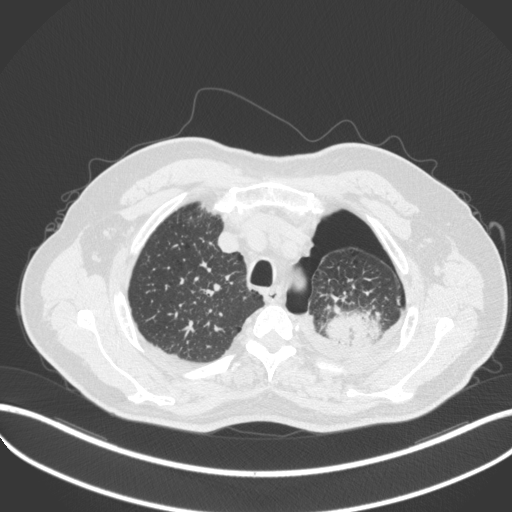
Chest CT, one axial slice. Position 412 of 466 along the scan axis. Lung window (W 1500 / L -600 HU). 1 mm slice thickness. 512 × 512 image matrix, field of view 400 × 400 mm. Male patient, age 76 years. Case-level facts recorded for this patient, not image findings: clinical TNM (as recorded): T3 N0 M1b.
Annotated regions visible in this slice (rectangle marked by the reading radiologist):
- lung tumour (recorded histology: adenocarcinoma): bounding box <315,302,385,347> (left, top, right, bottom; pixels)